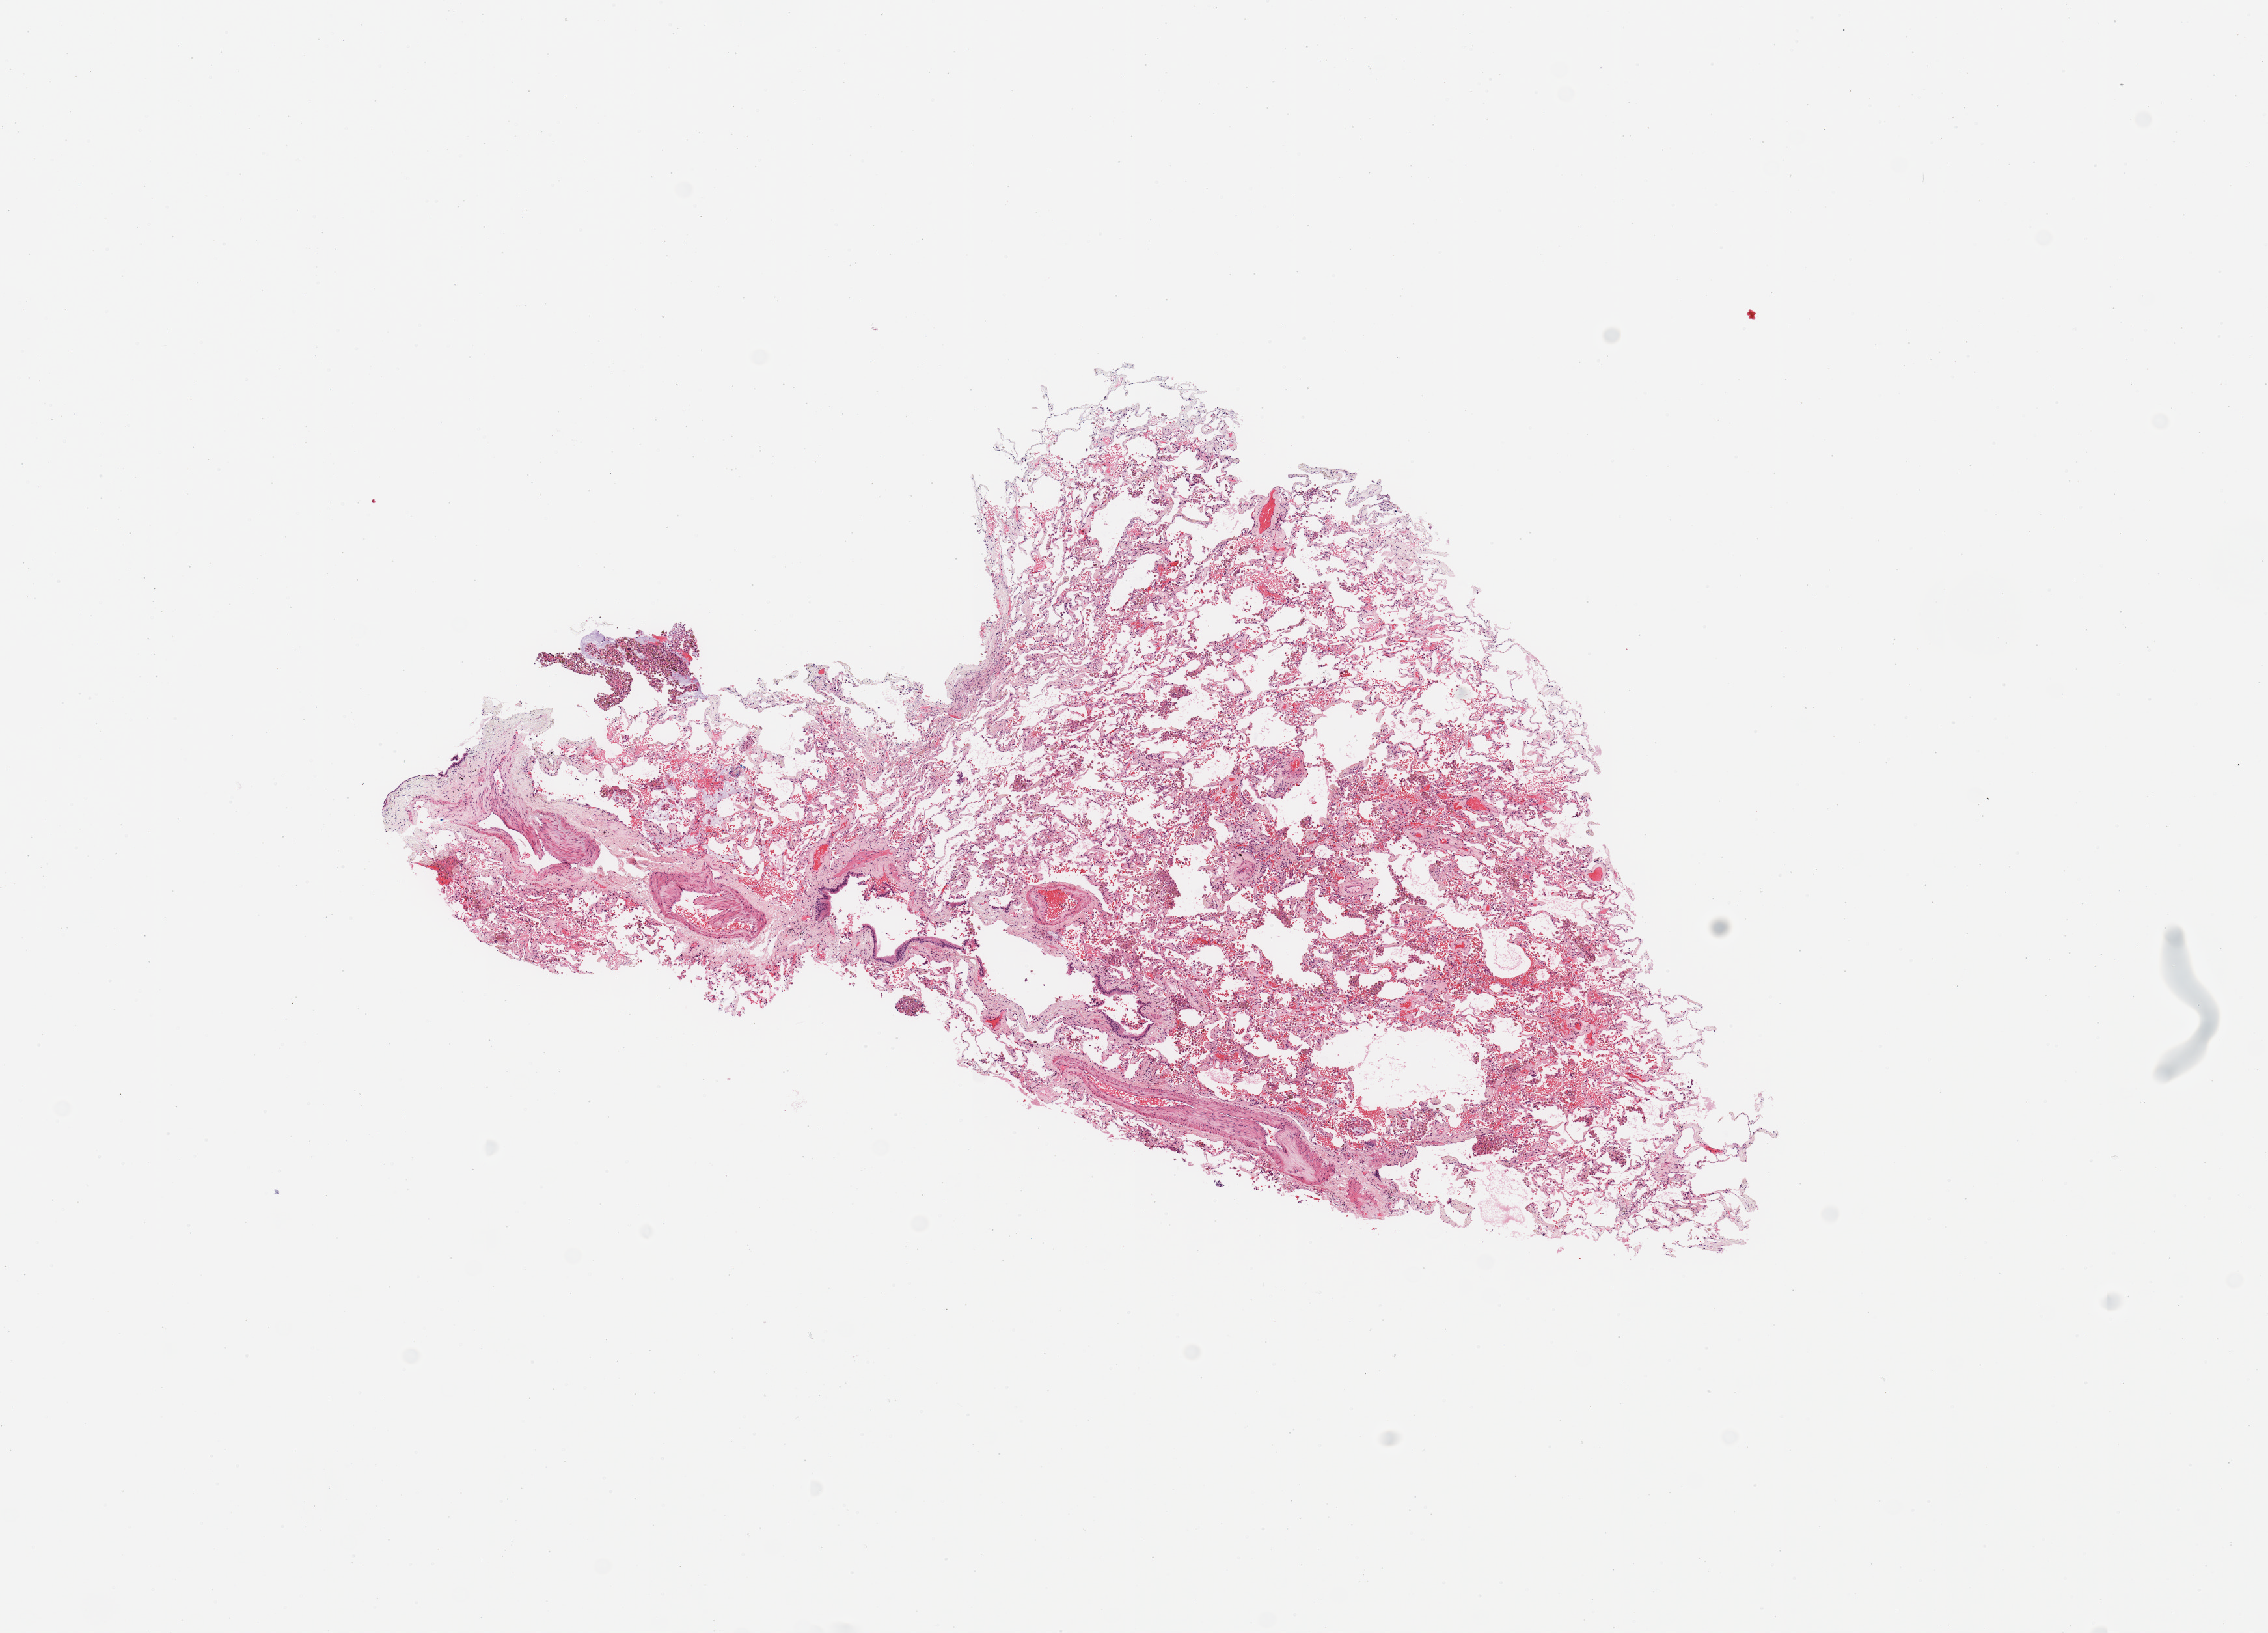
Digitized Hematoxylin and eosin (H&E) stained tissue section (whole slide), whole scanned area (about 13.8 x 9.9 mm, acquisition: 20x scan) shown as a low-resolution overview, normal (non-tumour) tissue sample, sampled site: lung. Patient: female, age 73 years.
This section: normal (non-tumour) tissue from the same patient. Patient diagnosis: Squamous cell carcinoma, NOS.